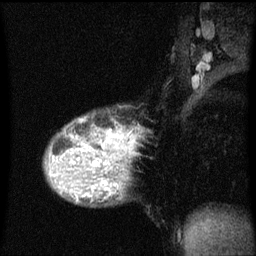
Breast MRI (dynamic contrast-enhanced), one sagittal slice. Slice 38 of 60 in the series (ordered by position). Dynamic contrast-enhanced series, image 2 of 3 at this slice position (ordered by acquisition). 1.5 T. TE 4.2 ms, TR 8 ms. 2 mm slice thickness. 256 × 256 image matrix, field of view 200 × 200 mm. Patient: female, 36 years.
Structures marked on this image (semi-automatic segmentation, software-assisted and operator-edited):
- analysis volume of interest (the breast-tissue region the enhancement analysis was run in; not a lesion): bounding box [x1, y1, x2, y2] px = [45, 118, 126, 169]
- tumour enhancement mask (voxels above the 70 % enhancement threshold inside the analysis volume of interest): [64, 120, 123, 169]